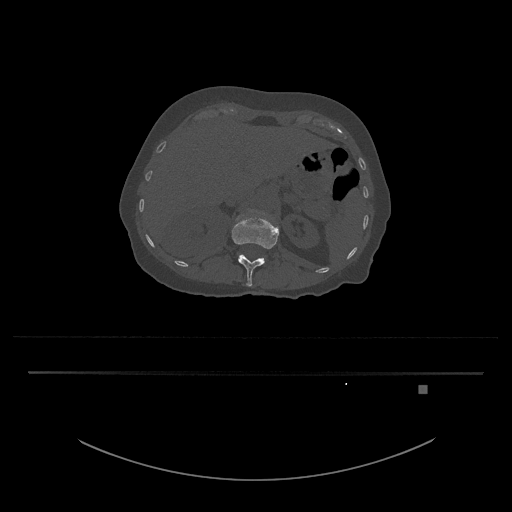
CT including the spine, one axial slice. Bone window (W 1800 / L 400 HU). 512 × 512 image matrix. Female patient, age 57 years. Case-level facts recorded for this patient, not image findings: primary cancer: cervical.
Annotated regions visible in this slice (semi-automatic segmentation, software-assisted and operator-edited):
- L1 vertebra: bounding box [x1, y1, x2, y2] px = [231, 217, 279, 287]